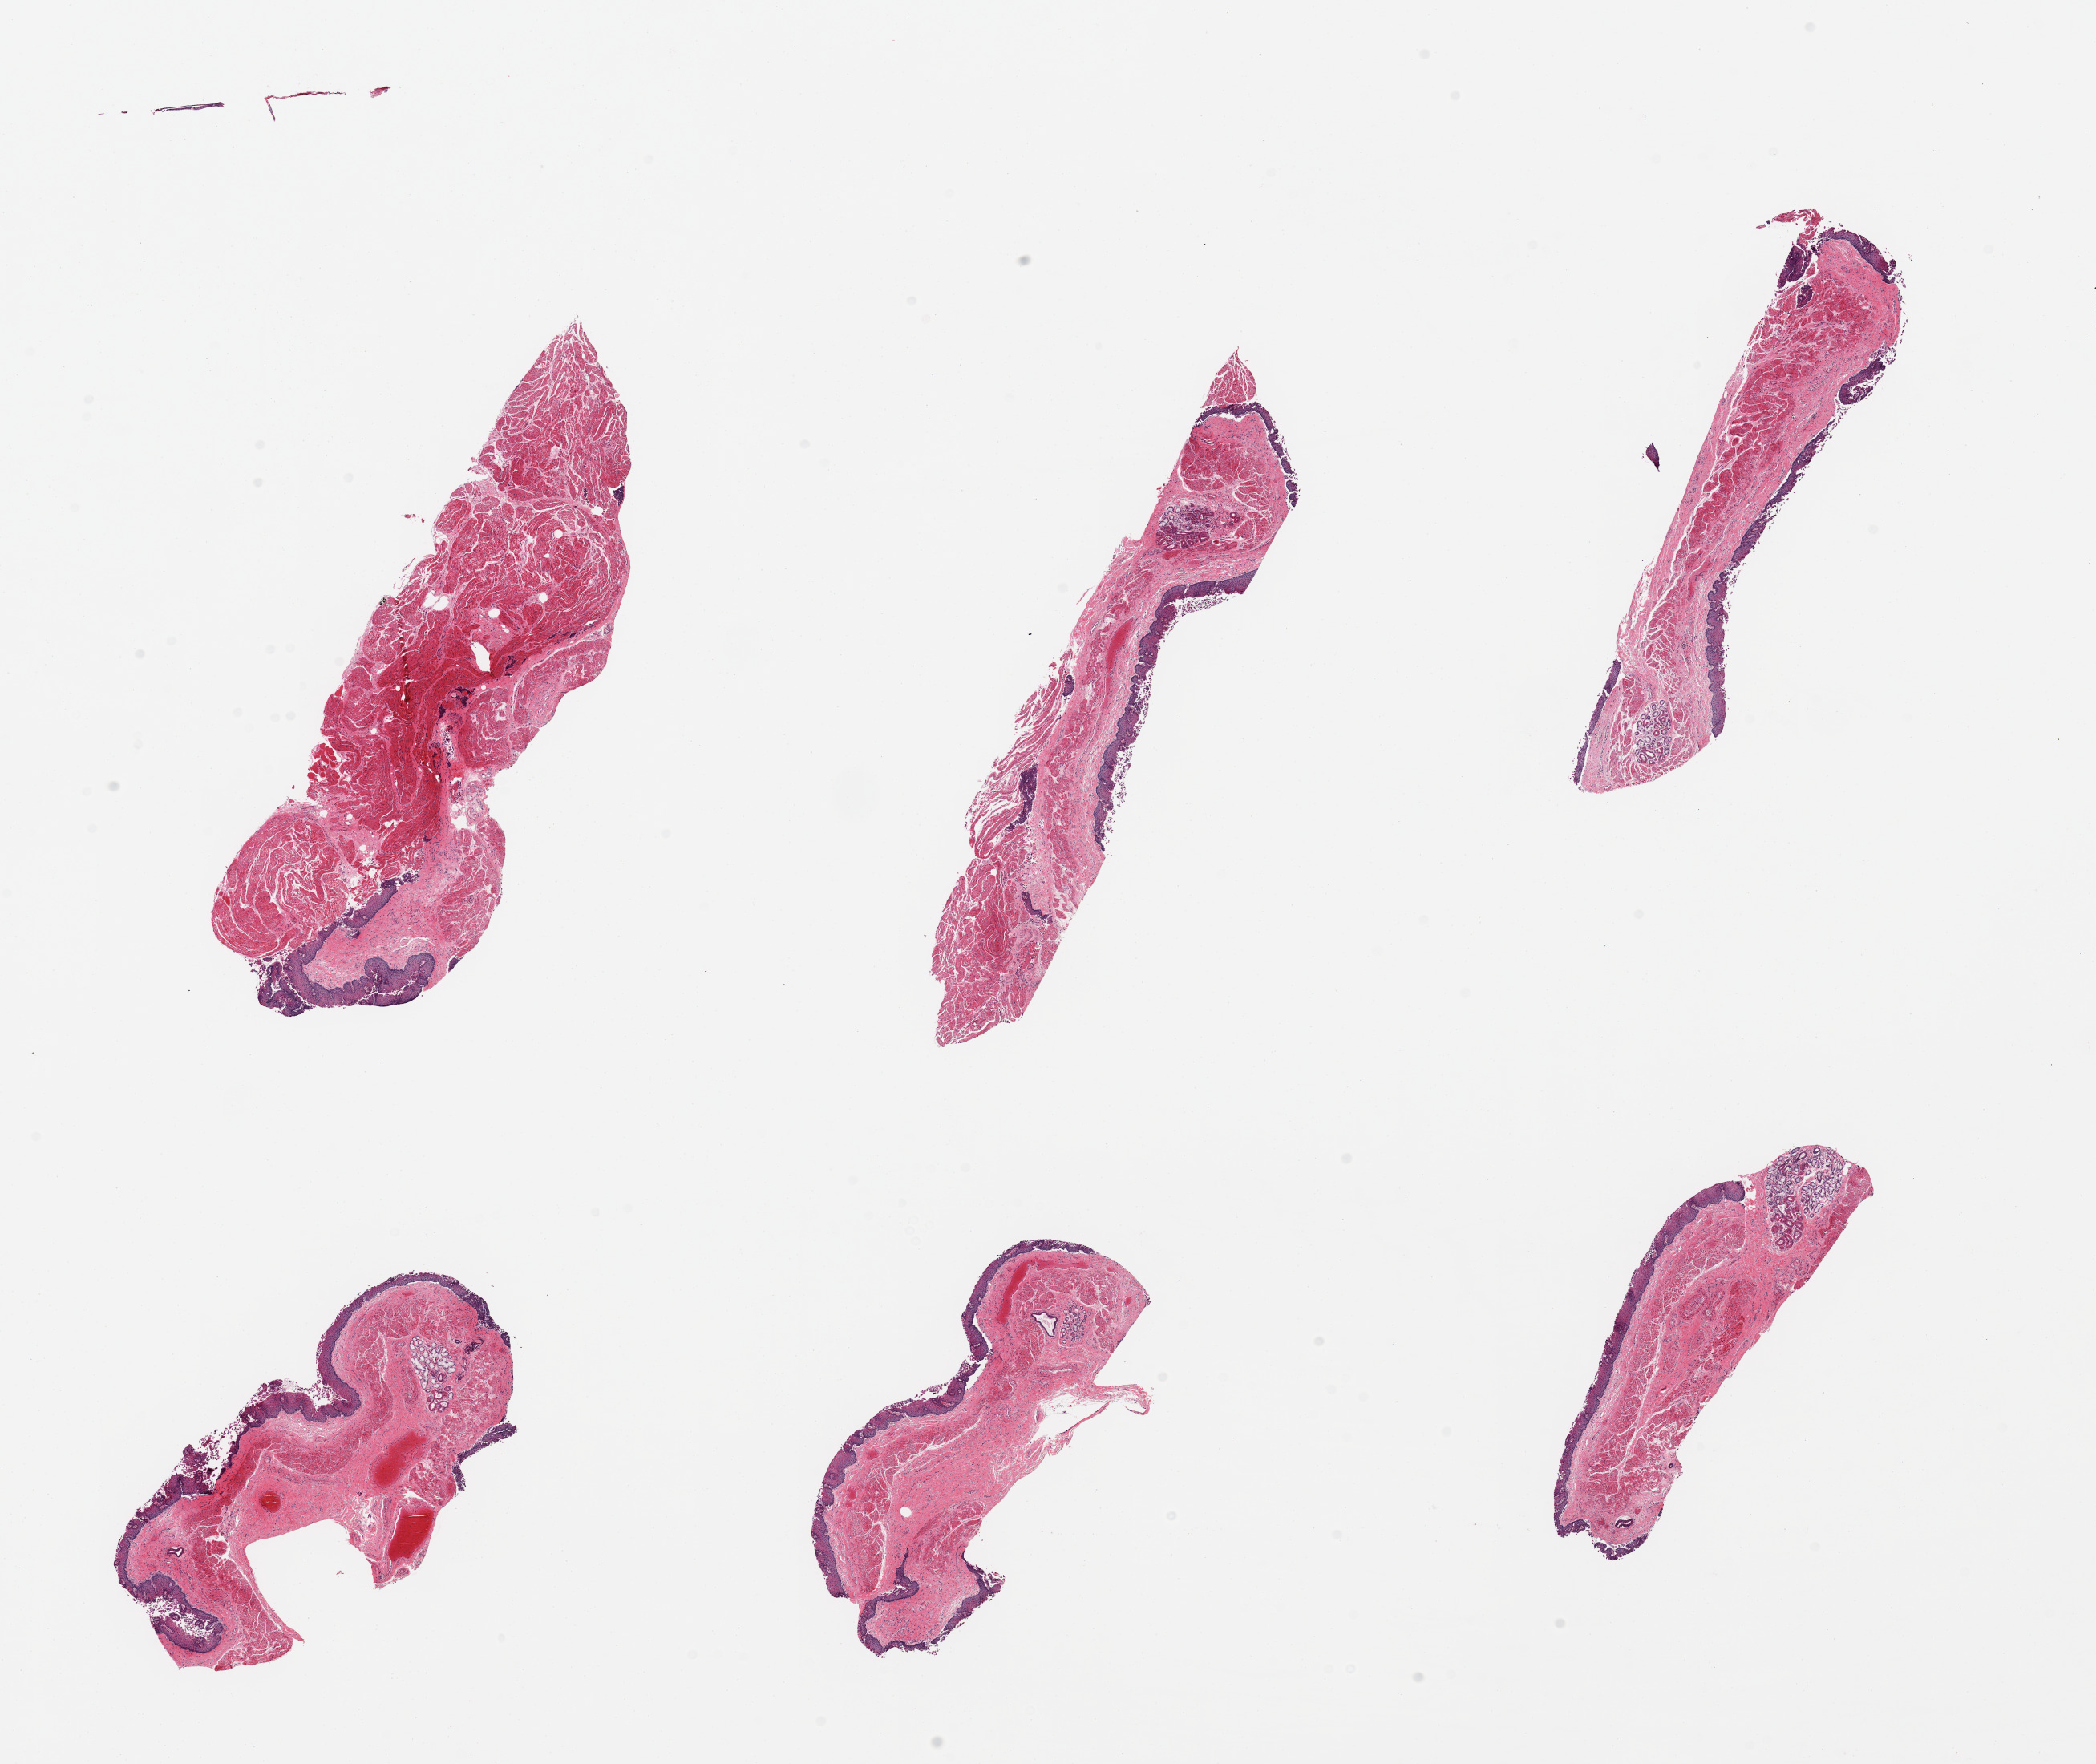
Digitized haematoxylin and eosin-stained section, brightfield — shown as a low-resolution overview of the whole scanned area (about 20.7 x 17.4 mm). PAXgene-fixed paraffin-embedded (PFPE) section. Target tissue: esophageal mucous membrane. Tissue donor sample. Male donor.
• reviewer comment on this tissue sample: 6 pieces; target squamous mucosa with sloughing surface measures up to ~ 0.18mm, 2 include muscularis (not target)